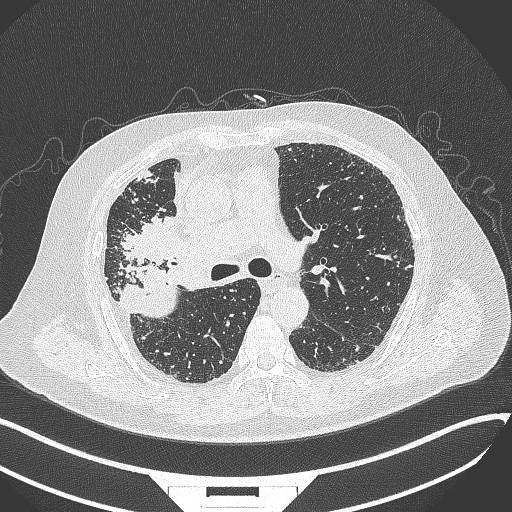
Chest CT, one axial slice. Position 215 of 384 along the scan axis. Reconstruction kernel B70f. 120 kVp. Lung window (W 1500 / L -600 HU). 1 mm slice thickness. 512 × 512 image matrix, field of view 400 × 400 mm. Male patient, age 69 years. Case-level facts recorded for this patient, not image findings: clinical TNM (as recorded): T4 N3 M1.
Annotated regions visible in this slice (rectangle marked by the reading radiologist):
- lung tumour (recorded histology: adenocarcinoma): box from (x=118, y=214) to (x=188, y=276) px